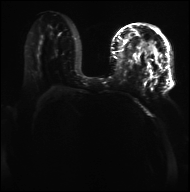
Breast MRI, one axial slice. Slice 15 of 36 in the series (ordered by position). Diffusion-weighted series; image 2 of 4 stored at this slice position (different b-values; order by instance number). 3 T. 4 mm slice thickness. 190 × 192 image matrix, field of view 317 × 320 mm. Female patient.
Outlined on this slice (manually delineated by an expert):
- tumour on diffusion-weighted imaging: bounding box [x1, y1, x2, y2] px = [47, 41, 71, 56]